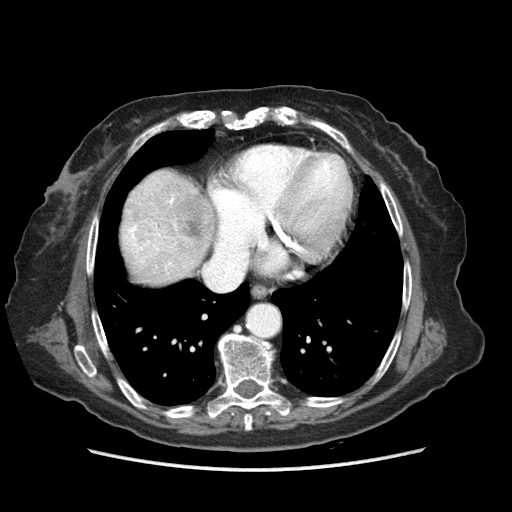
Contrast-enhanced abdominal CT (liver protocol), one axial slice. Position 78 of 89 along the scan axis. Reconstruction kernel STANDARD. Soft-tissue window (W 400 / L 40 HU). 2.5 mm slice thickness. 512 × 512 image matrix. Case-level facts recorded for this patient, not image findings: diagnosis: hepatocellular carcinoma (patient treated with transarterial chemoembolisation; whether this scan precedes or follows treatment is not stated here); TNM stage (as recorded): Stage-IIIA; Child-Pugh class: A; tumour differentiation: well differentiated.
Outlined on this slice (semi-automatically segmented with operator editing):
- liver parenchyma outside the tumour (the mass and vessels are separate outlines, so this box may not span the whole liver): bounding box (x1, y1, x2, y2) in pixels: (120, 170, 214, 284)
- mass: (145, 214, 203, 237)
- liver vessels: (126, 198, 174, 264)